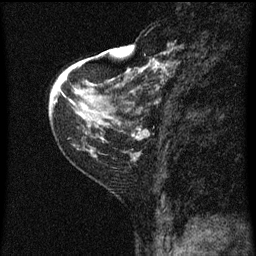
Breast MRI (dynamic contrast-enhanced), one sagittal slice; position 18 of 60 along the scan axis; dynamic contrast-enhanced series, image 2 of 3 at this slice position (ordered by acquisition); 1.5 T; TE 4.2 ms, TR 8 ms; 256 × 256 image matrix, field of view 180 × 180 mm. Patient: female, 48 years.
Outlined on this slice (semi-automatically segmented with operator editing):
- analysis volume of interest (the breast-tissue region the enhancement analysis was run in; not a lesion): box from (x=128, y=54) to (x=175, y=125) px
- tumour enhancement mask (voxels above the 70 % enhancement threshold inside the analysis volume of interest): (x=131, y=54)–(x=169, y=103)